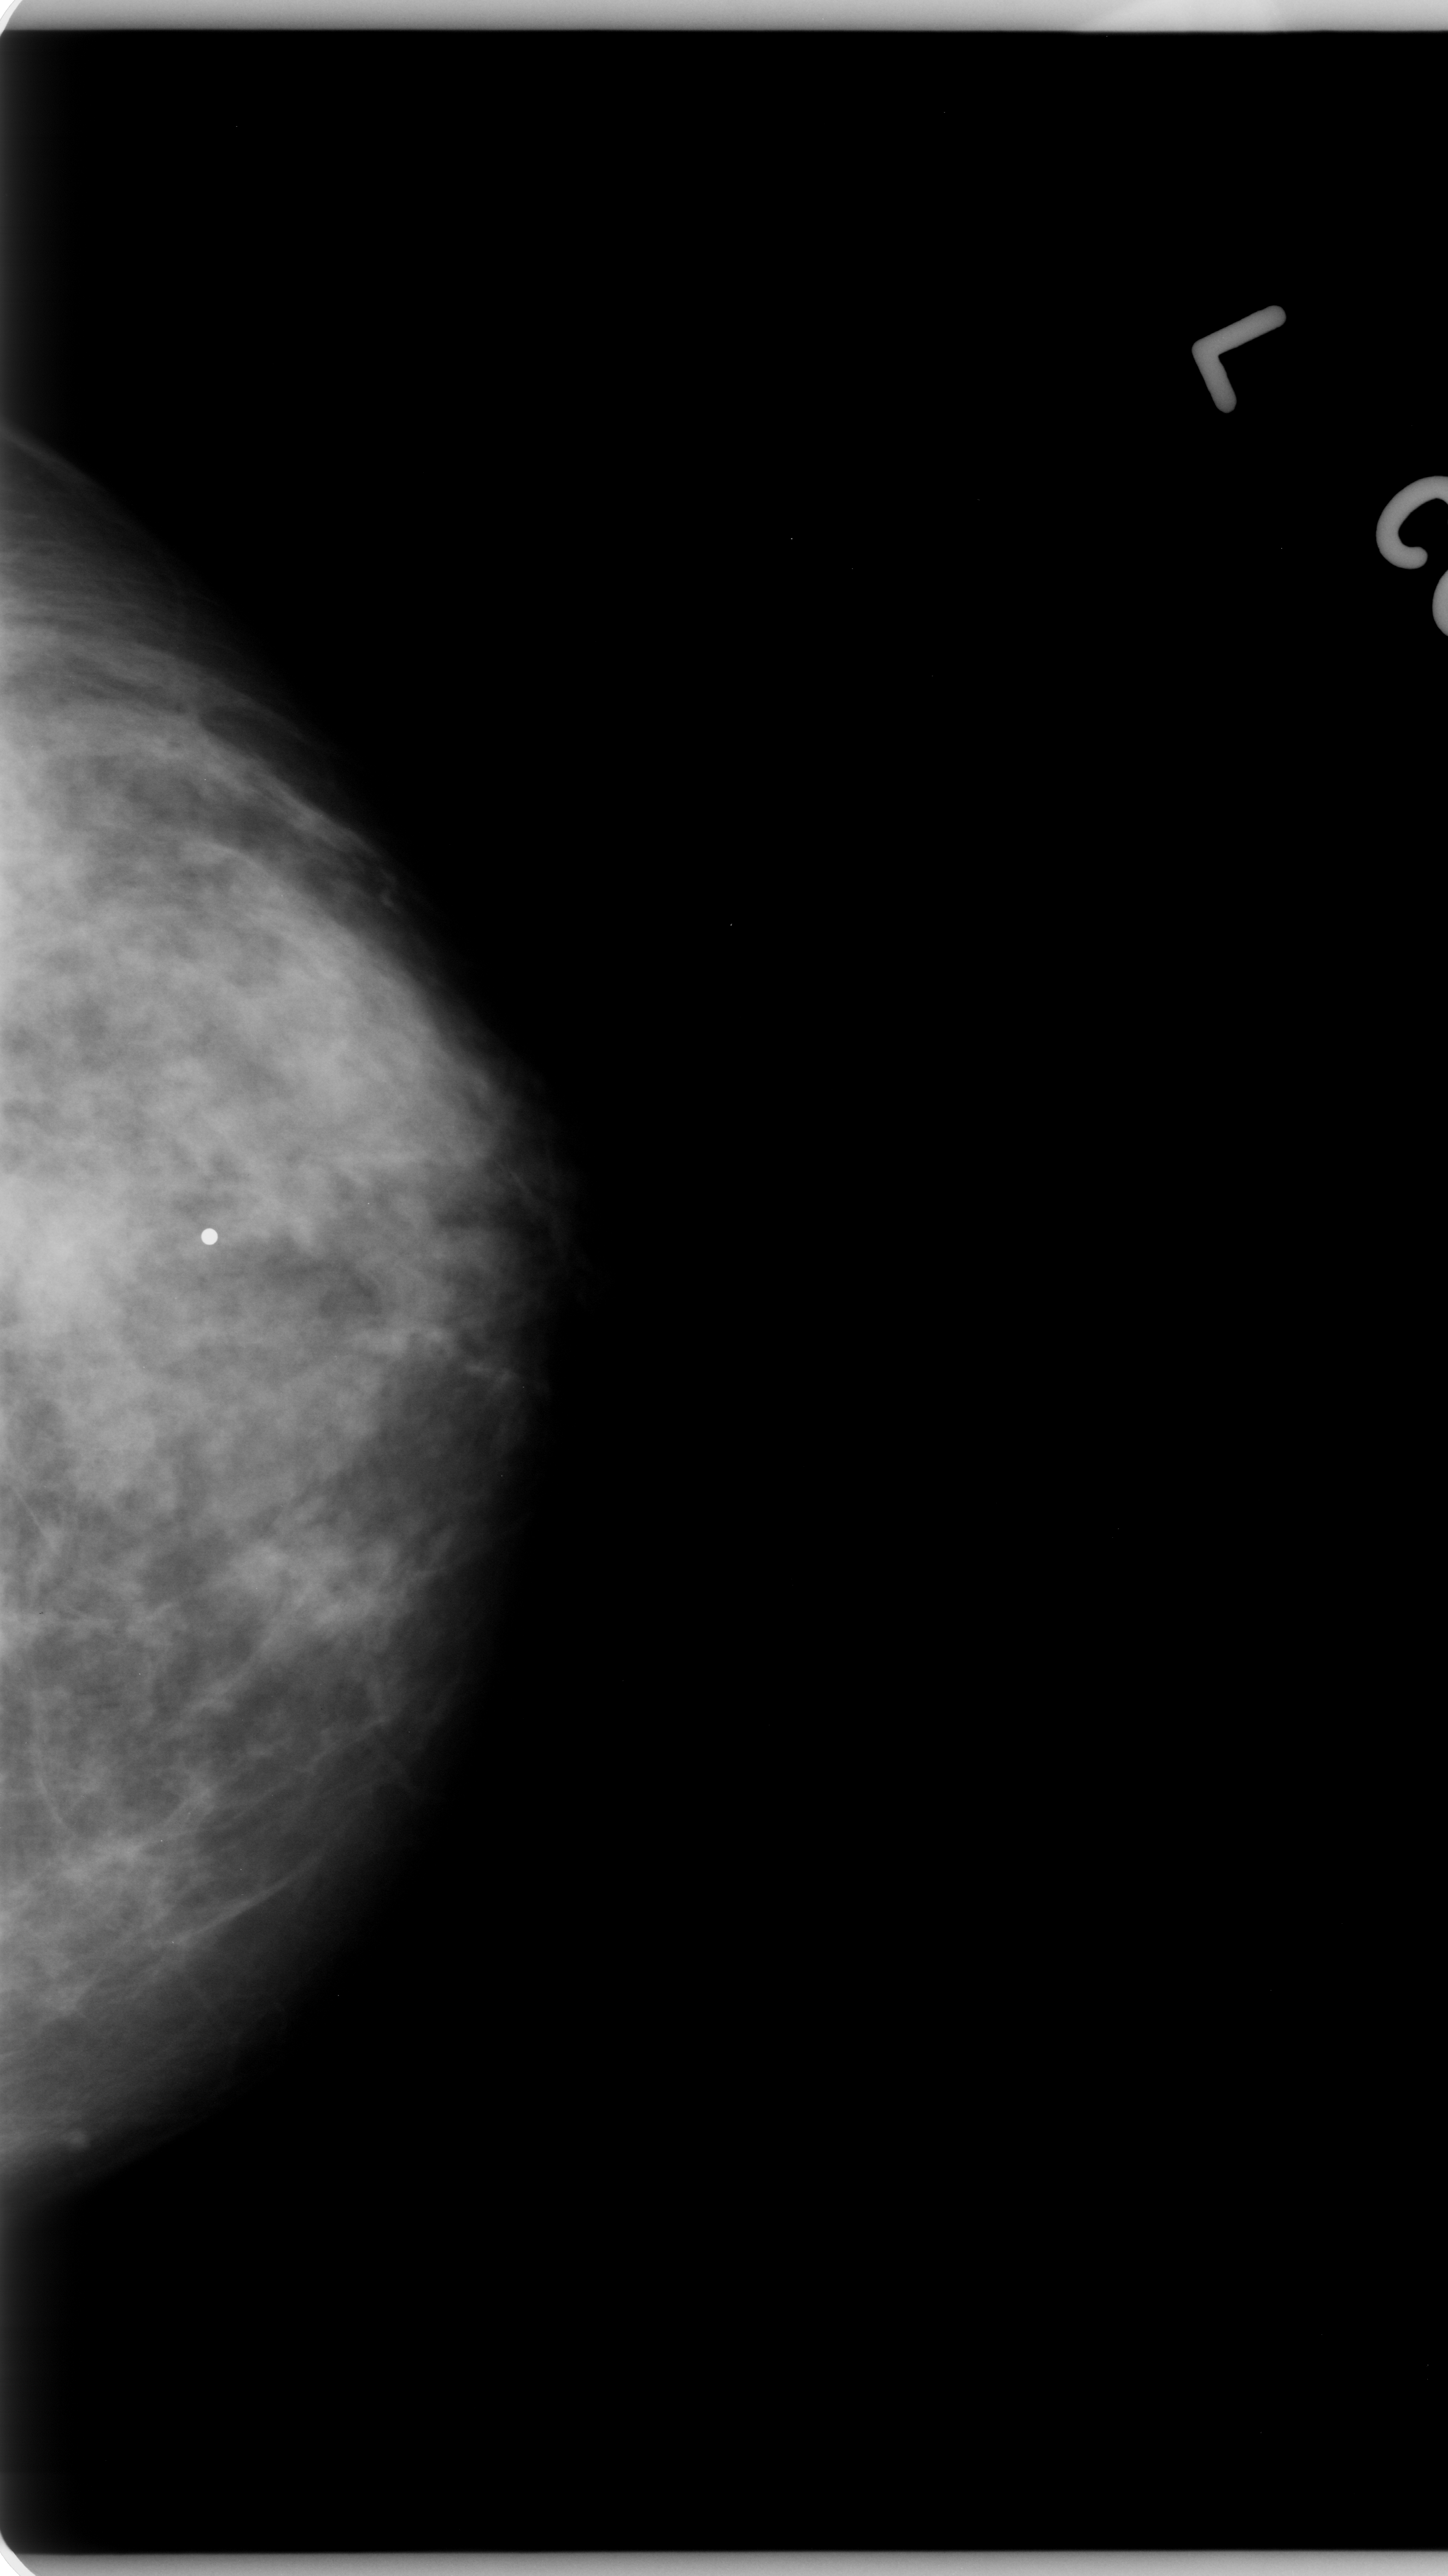
Scanned film-screen mammogram. Left breast. Craniocaudal (CC) view. 1448 × 2576 image matrix.
Expert-marked regions of interest on this film, with their recorded descriptors:
- mass, shape lobulated, margins ill defined; BI-RADS assessment category 4; subtlety rating 1 on a 1 (subtle) to 5 (obvious) scale; pathology (as recorded): malignant: bounding box <14,1163,152,1352> (left, top, right, bottom; pixels)